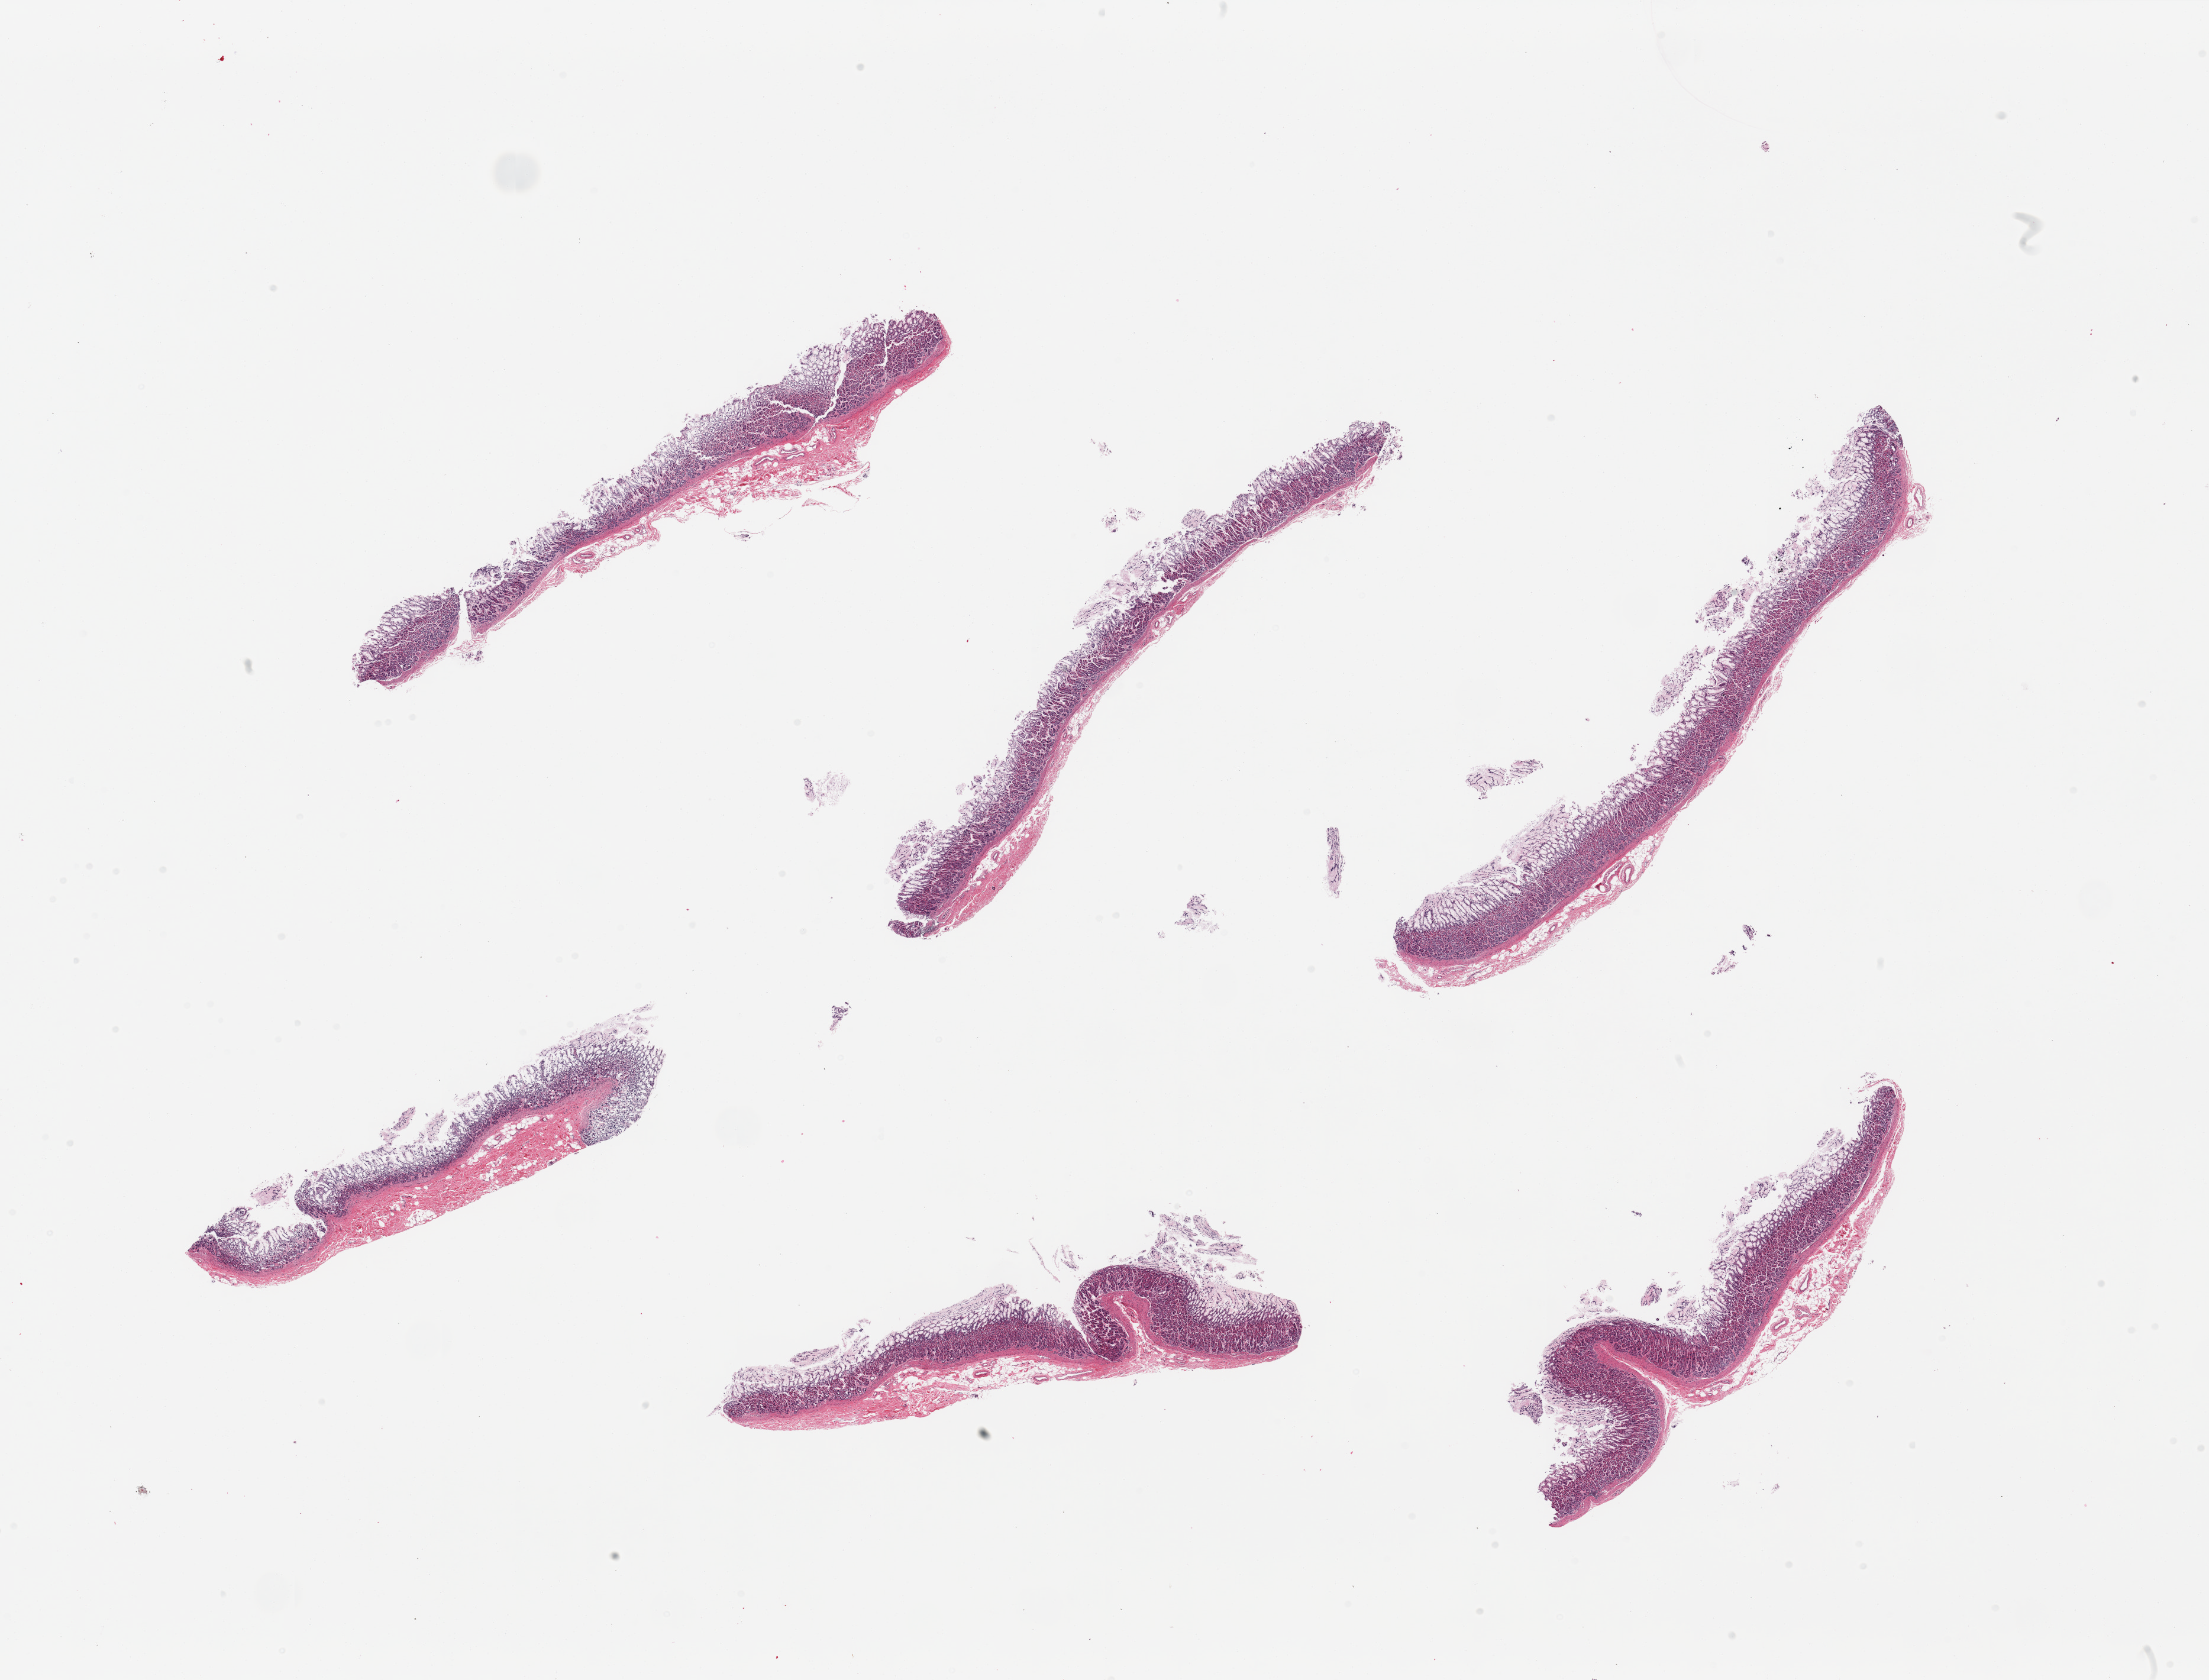
Digitized hematoxylin and eosin (H&E)-stained section — shown as a low-resolution overview of the whole scanned area (about 29.5 x 22.5 mm, acquisition: 20x scan). PAXgene-fixed paraffin-embedded (PFPE) section. Target tissue: stomach. Tissue donor sample. Female donor.
Pathologist's review note for this sample: 6 pieces; all have mucosa only, no muscularis.